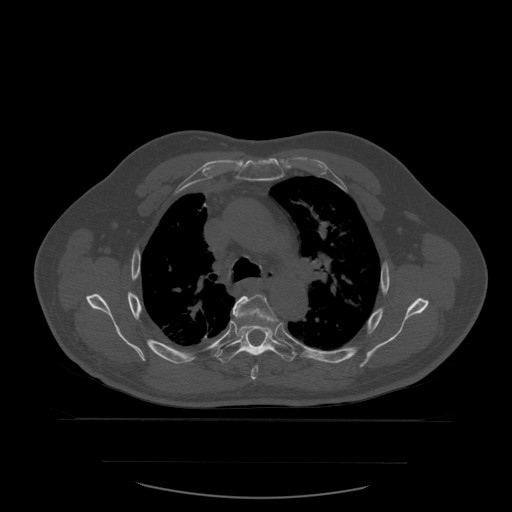
CT including the spine, one axial slice. Position 413 of 590 along the scan axis. Bone window (W 1800 / L 400 HU). 512 × 512 image matrix, field of view 479 × 479 mm. Patient age 71 years. Case-level facts recorded for this patient, not image findings: primary cancer: lung; vertebrae with lytic lesions (as recorded): T1, T2, L5, S1.
Annotated regions visible in this slice (semi-automatically segmented with operator editing):
- T5 vertebra: bounding box [x1, y1, x2, y2] px = [234, 295, 277, 380]
- T6 vertebra: [217, 308, 296, 364]